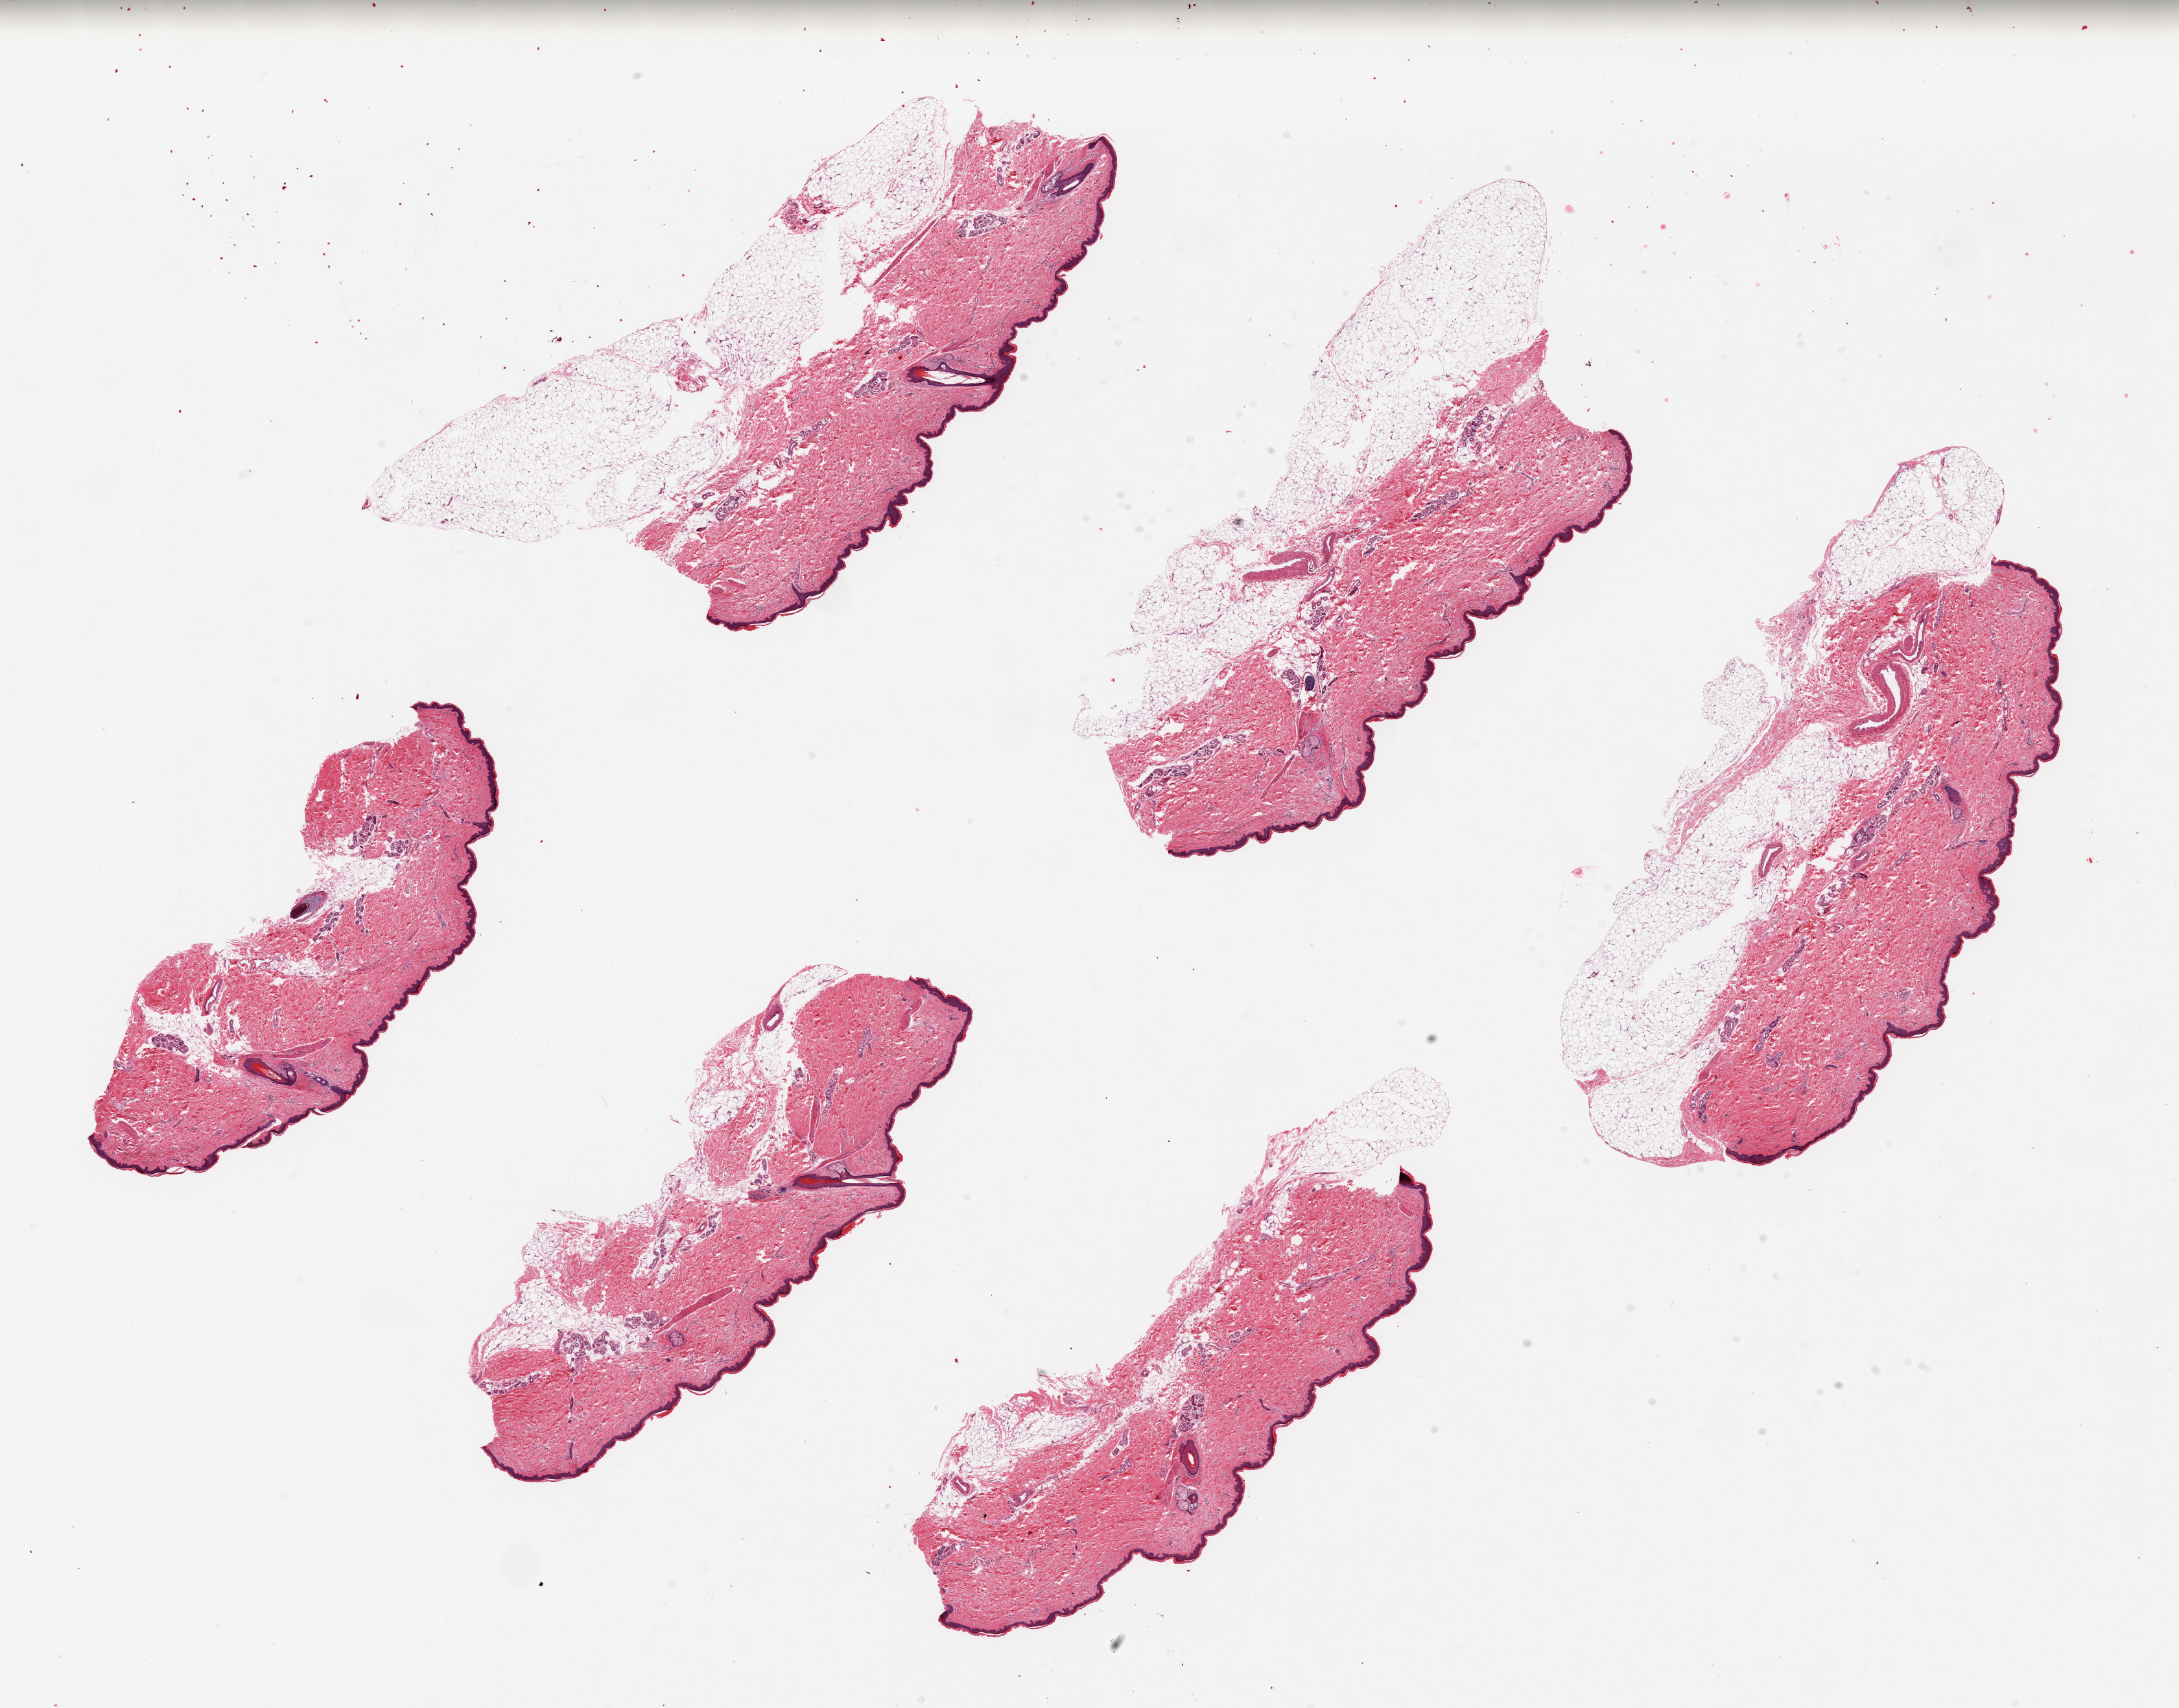
Digitized hematoxylin and eosin (H&E)-stained section, brightfield, a low-resolution overview of the entire scanned area, about 26.6 x 20.8 mm; PAXgene-fixed paraffin-embedded (PFPE) section; section of skin of lower leg (target tissue); donor tissue sample. Donor sex: male.
Reviewer comment on this tissue sample: 6 ~7.5x2.5mm pieces. Squamous epithelium is ~1-2% of thickness; several pieces have adherent aggregates of subcutaneous fat up to ~9x2mm.